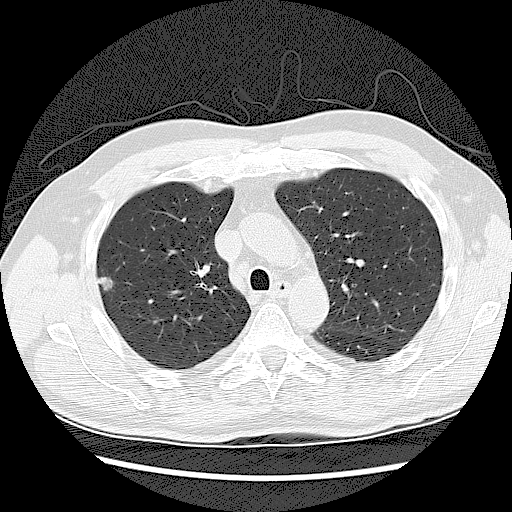
Low-dose screening chest CT, axial slice; second screening round (one year after baseline); lung window (W 1500 / L -600 HU); slice 37 of 120 in the series. Male participant, aged 62 years at enrolment.
Expert reader's lesion annotation, bounding box <89,270,118,296> (left, top, right, bottom; pixels). Screening reader's record for this exam (one nodule recorded; not confirmed to be the boxed lesion): non-calcified nodule or mass ≥4 mm, right upper lobe, 10 × 10 mm, smooth margins, soft tissue attenuation, pre-existing on the prior screen: yes; interval growth: yes. Official screen result: positive, other.